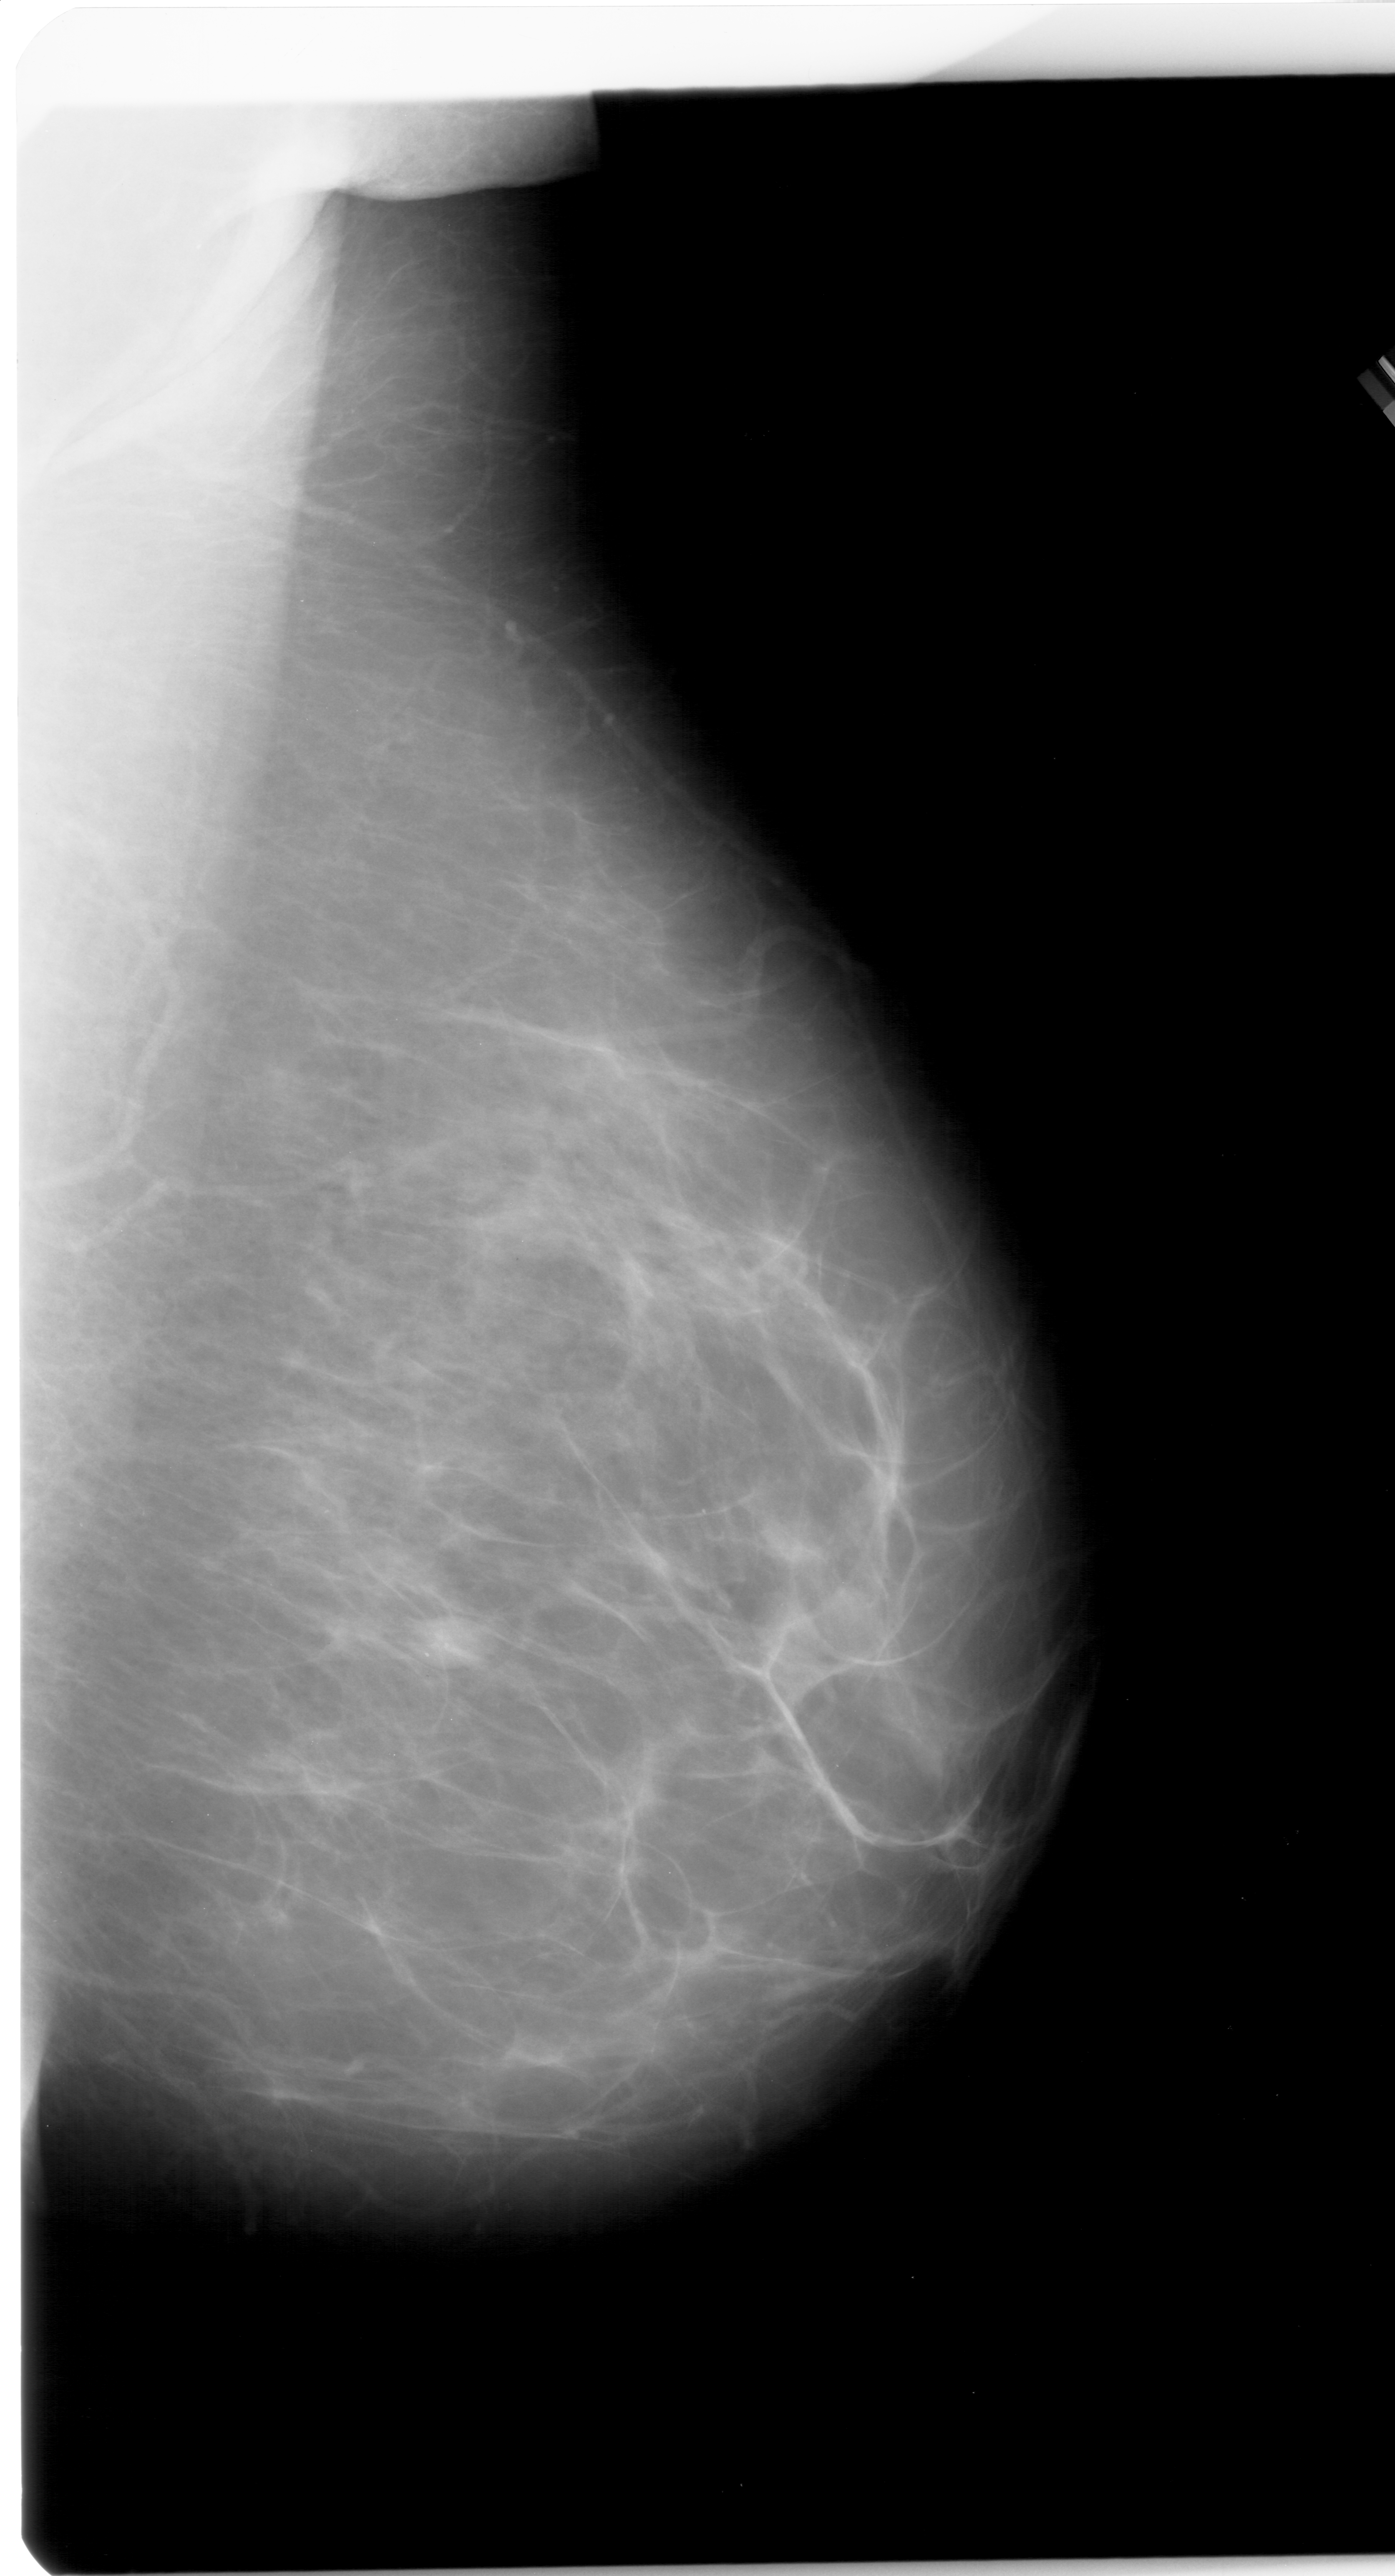
Mammogram (digitized film); right breast; MLO view; BI-RADS breast density category 2 (scale 1–4).
- Marked abnormality: mass, shape oval, margins circumscribed; BI-RADS assessment category 3; subtlety rating 4 on a 1 (subtle) to 5 (obvious) scale; pathology result (as recorded, not read from the image): benign.